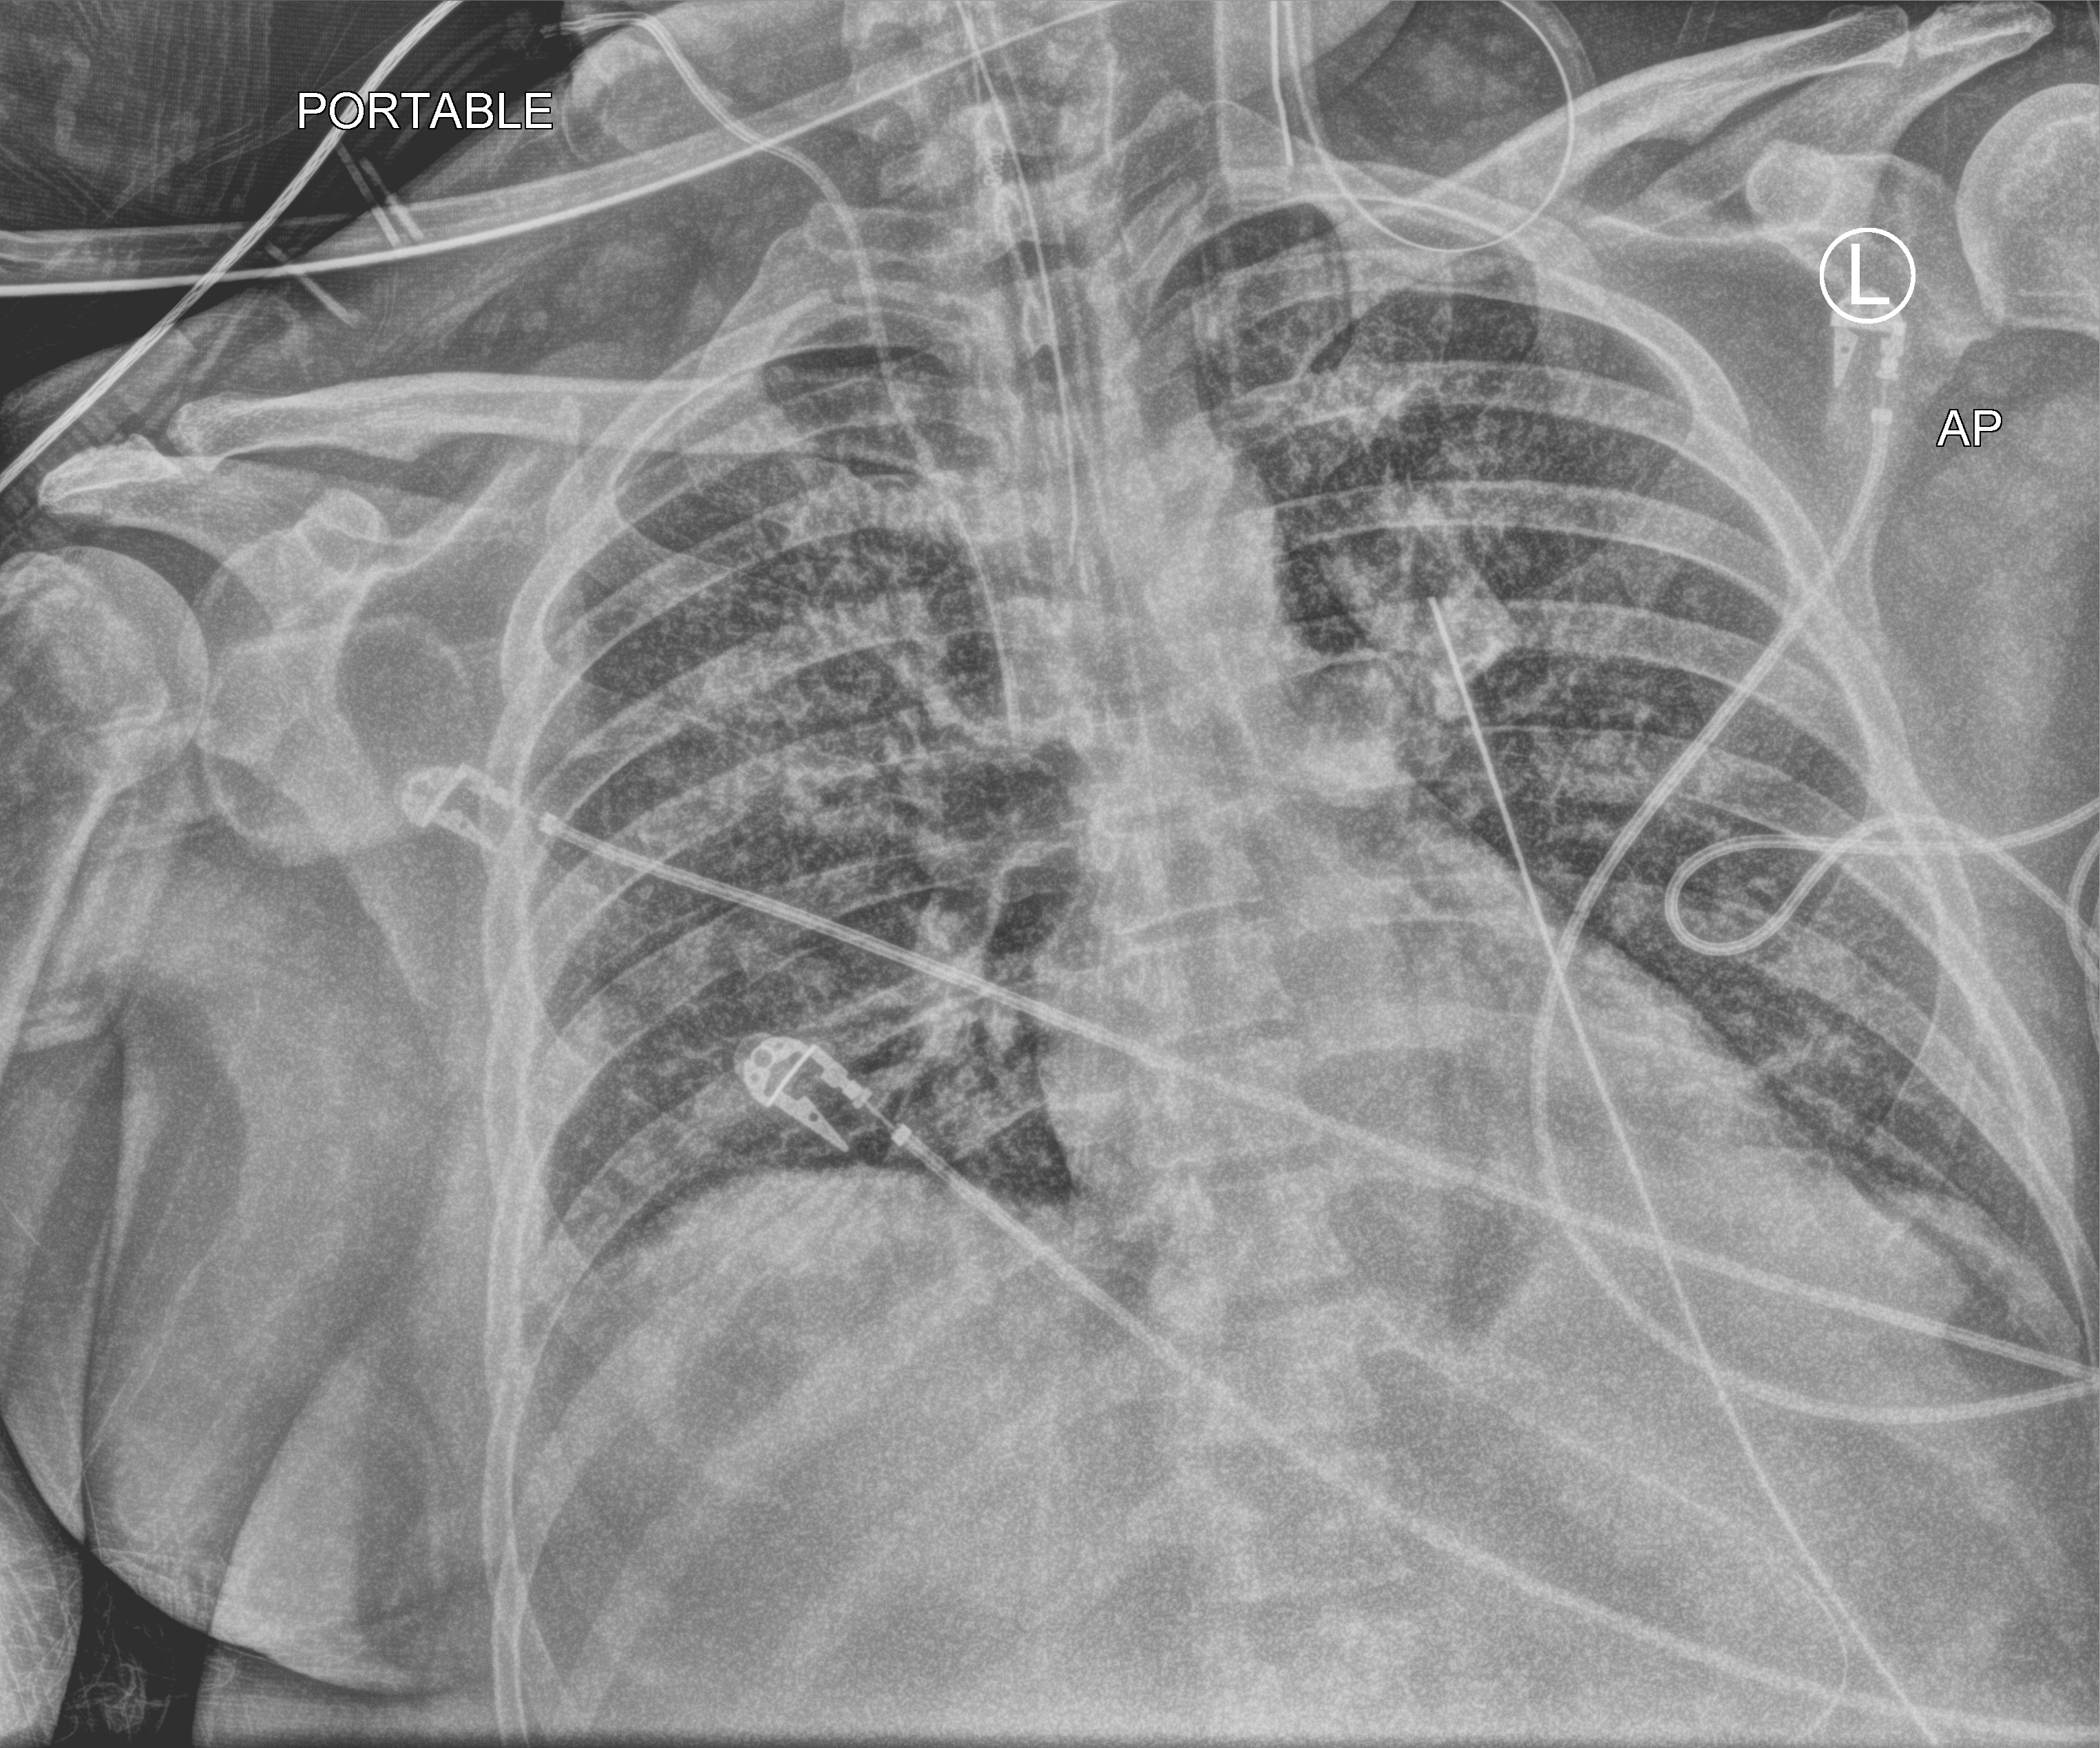
Chest X-ray (portable), anteroposterior (AP) projection. Patient hospitalised with COVID-19; male, aged 18–59 years.
From the hospital-stay record, not from the radiograph (when in the stay this image was taken is not recorded):
- admitted to intensive care during this hospital stay: yes